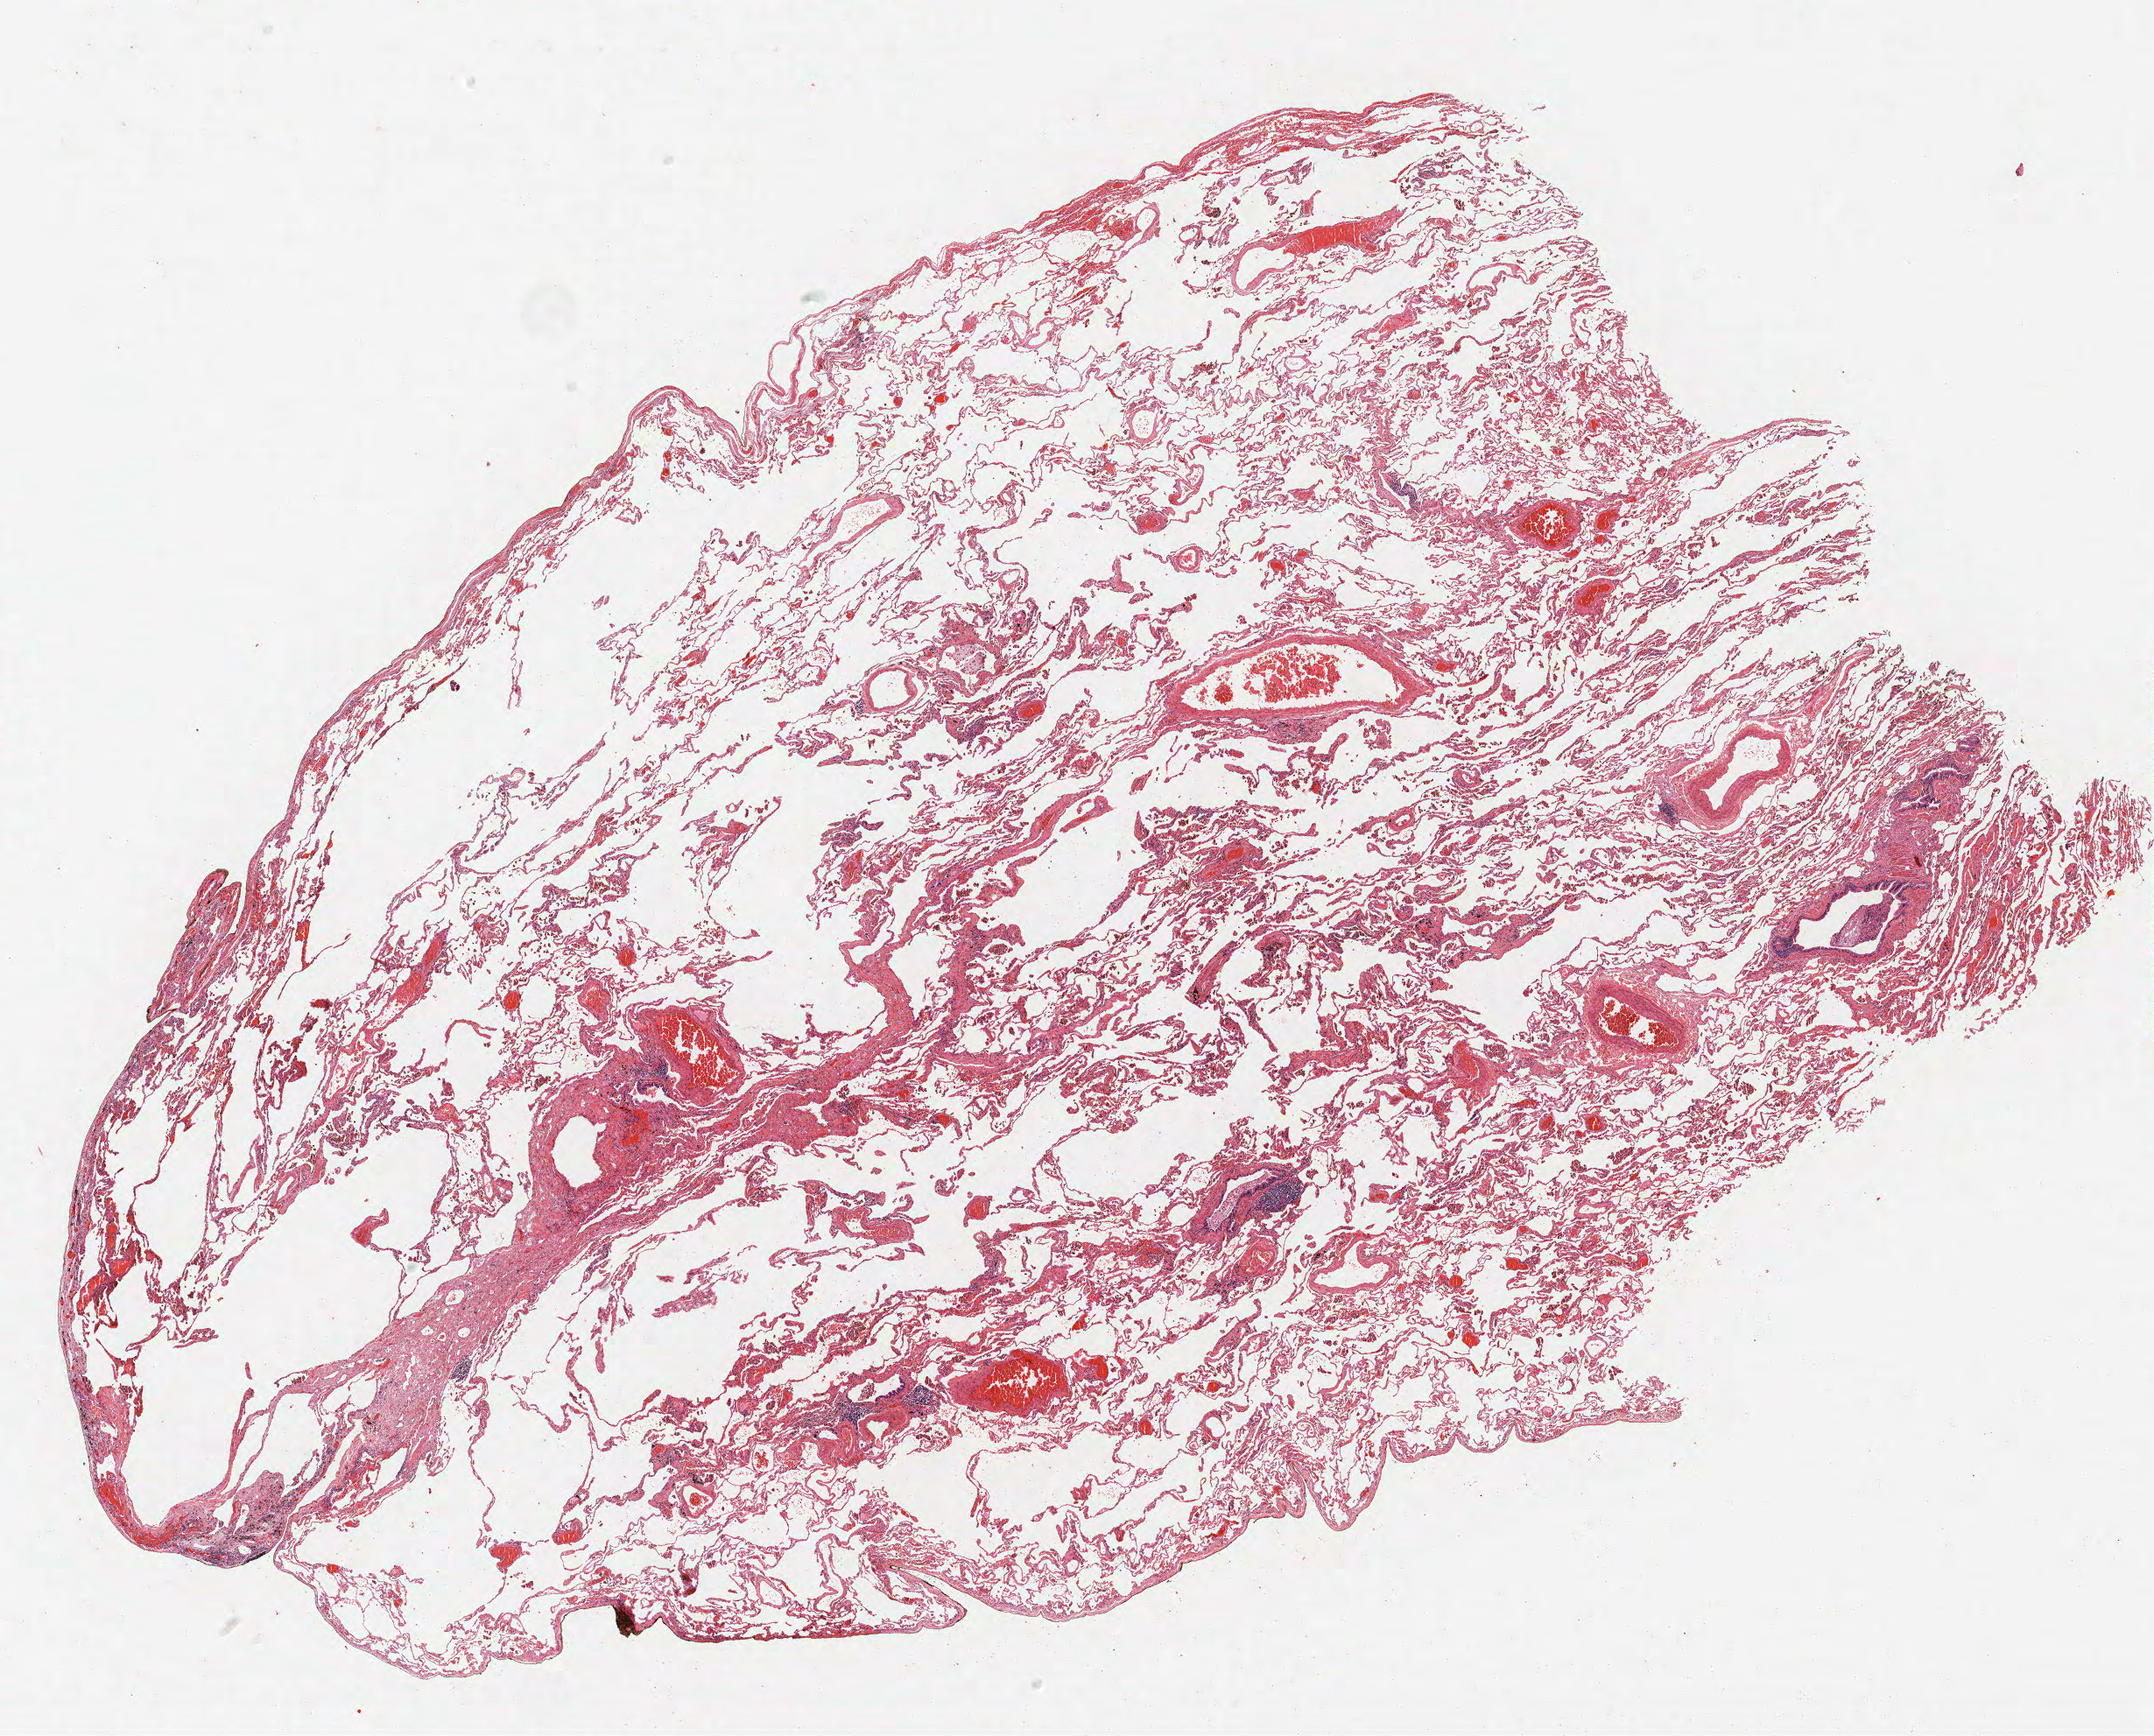
Whole-slide histology image, H&E — low-resolution overview of the scanned area, about 19.7 x 15.9 mm; FFPE section; lung. Female patient, aged 67 at enrolment. Current smoker at enrolment. Grade: poorly differentiated (G3).
ICD-O-3 topography: upper lobe of lung (C34.1). Tumour size (pathology): 13 mm. Participant's lung-cancer diagnosis: Adenocarcinoma, NOS (ICD-O-3 8140/3). Primary tumour location (clinical record): left upper lobe. Stage (AJCC 6th edition): IA.